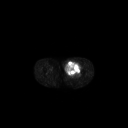
FDG PET of an extremity soft-tissue mass (from a PET/CT study), one axial slice; slice 240 of 267 in the series (ordered by position); 128 × 128 image matrix, field of view 700 × 700 mm. Male patient, age 63 years. Case-level facts recorded for this patient, not image findings: histological type: pleiomorphic liposarcoma; grade: high; site of the primary tumour: left thigh.
Outlined on this slice (expert contour drawn on MRI and transferred to this co-registered scan by the dataset authors):
- gross tumour volume including surrounding oedema: bounding box [x1, y1, x2, y2] px = [65, 60, 82, 76]
- gross tumour volume (mass): [65, 60, 81, 76]